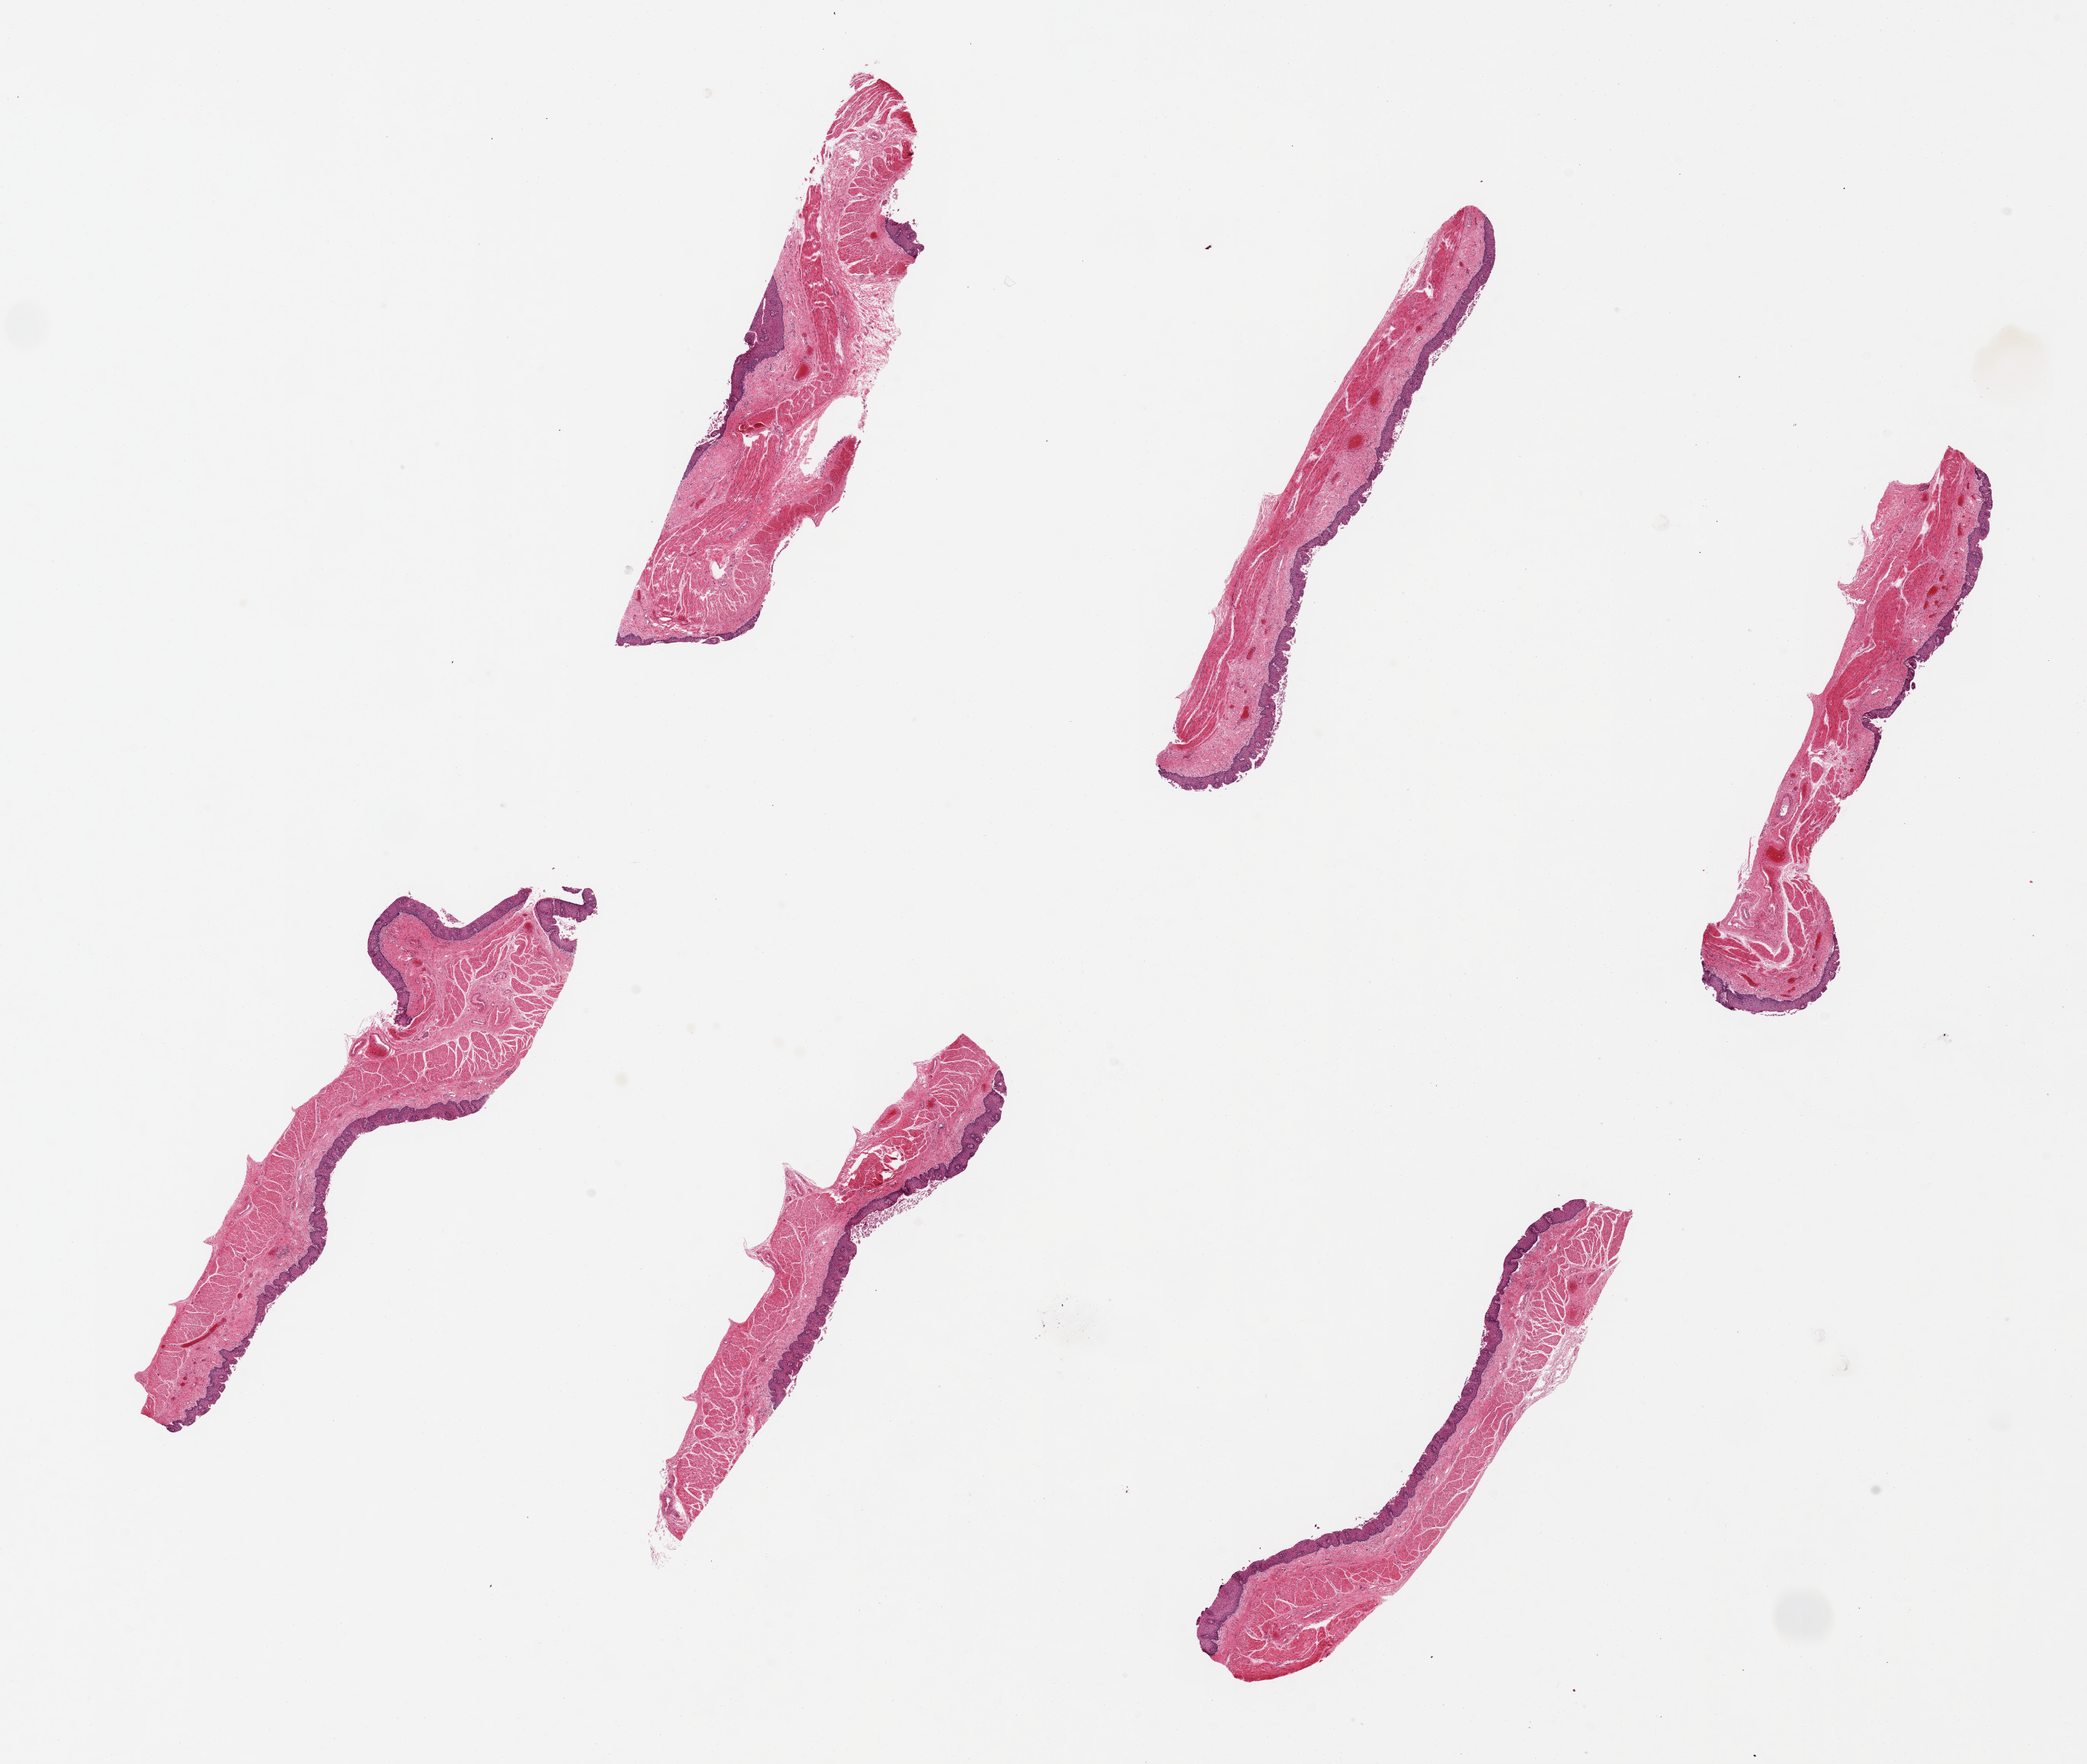
Hematoxylin and eosin (H&E) whole-slide image, brightfield, low-resolution overview of the scanned area, about 21.7 x 18.3 mm (slide scanned at 20x); PAXgene-fixed paraffin-embedded (PFPE) section; section of esophageal mucous membrane (target tissue); donor tissue sample. Donor sex: female.
Review note (as recorded): 6 pieces up to 6.6x1 mm; focal epithelial sloughing.